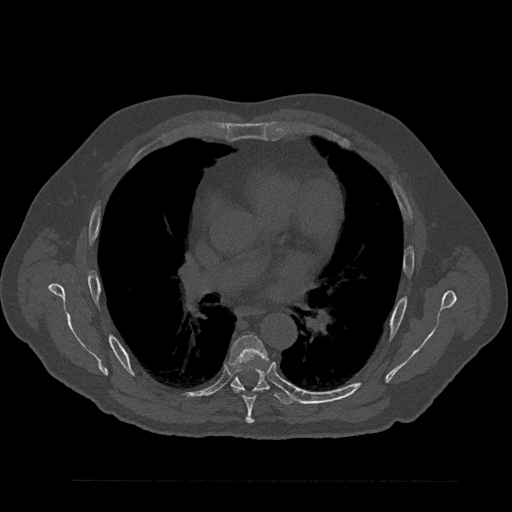
CT including the spine, one axial slice; slice 533 of 797 in the series (ordered by position); reconstruction kernel Br40s/3; bone window (W 1800 / L 400 HU); 0.5 mm slice thickness; 512 × 512 image matrix, field of view 430 × 430 mm. Male patient, age 61 years. Case-level facts recorded for this patient, not image findings: primary cancer: prostate.
Outlined on this slice (semi-automatic segmentation, software-assisted and operator-edited):
- T6 vertebra: bounding box (x1, y1, x2, y2) in pixels: (229, 335, 268, 424)
- T7 vertebra: (231, 368, 293, 405)